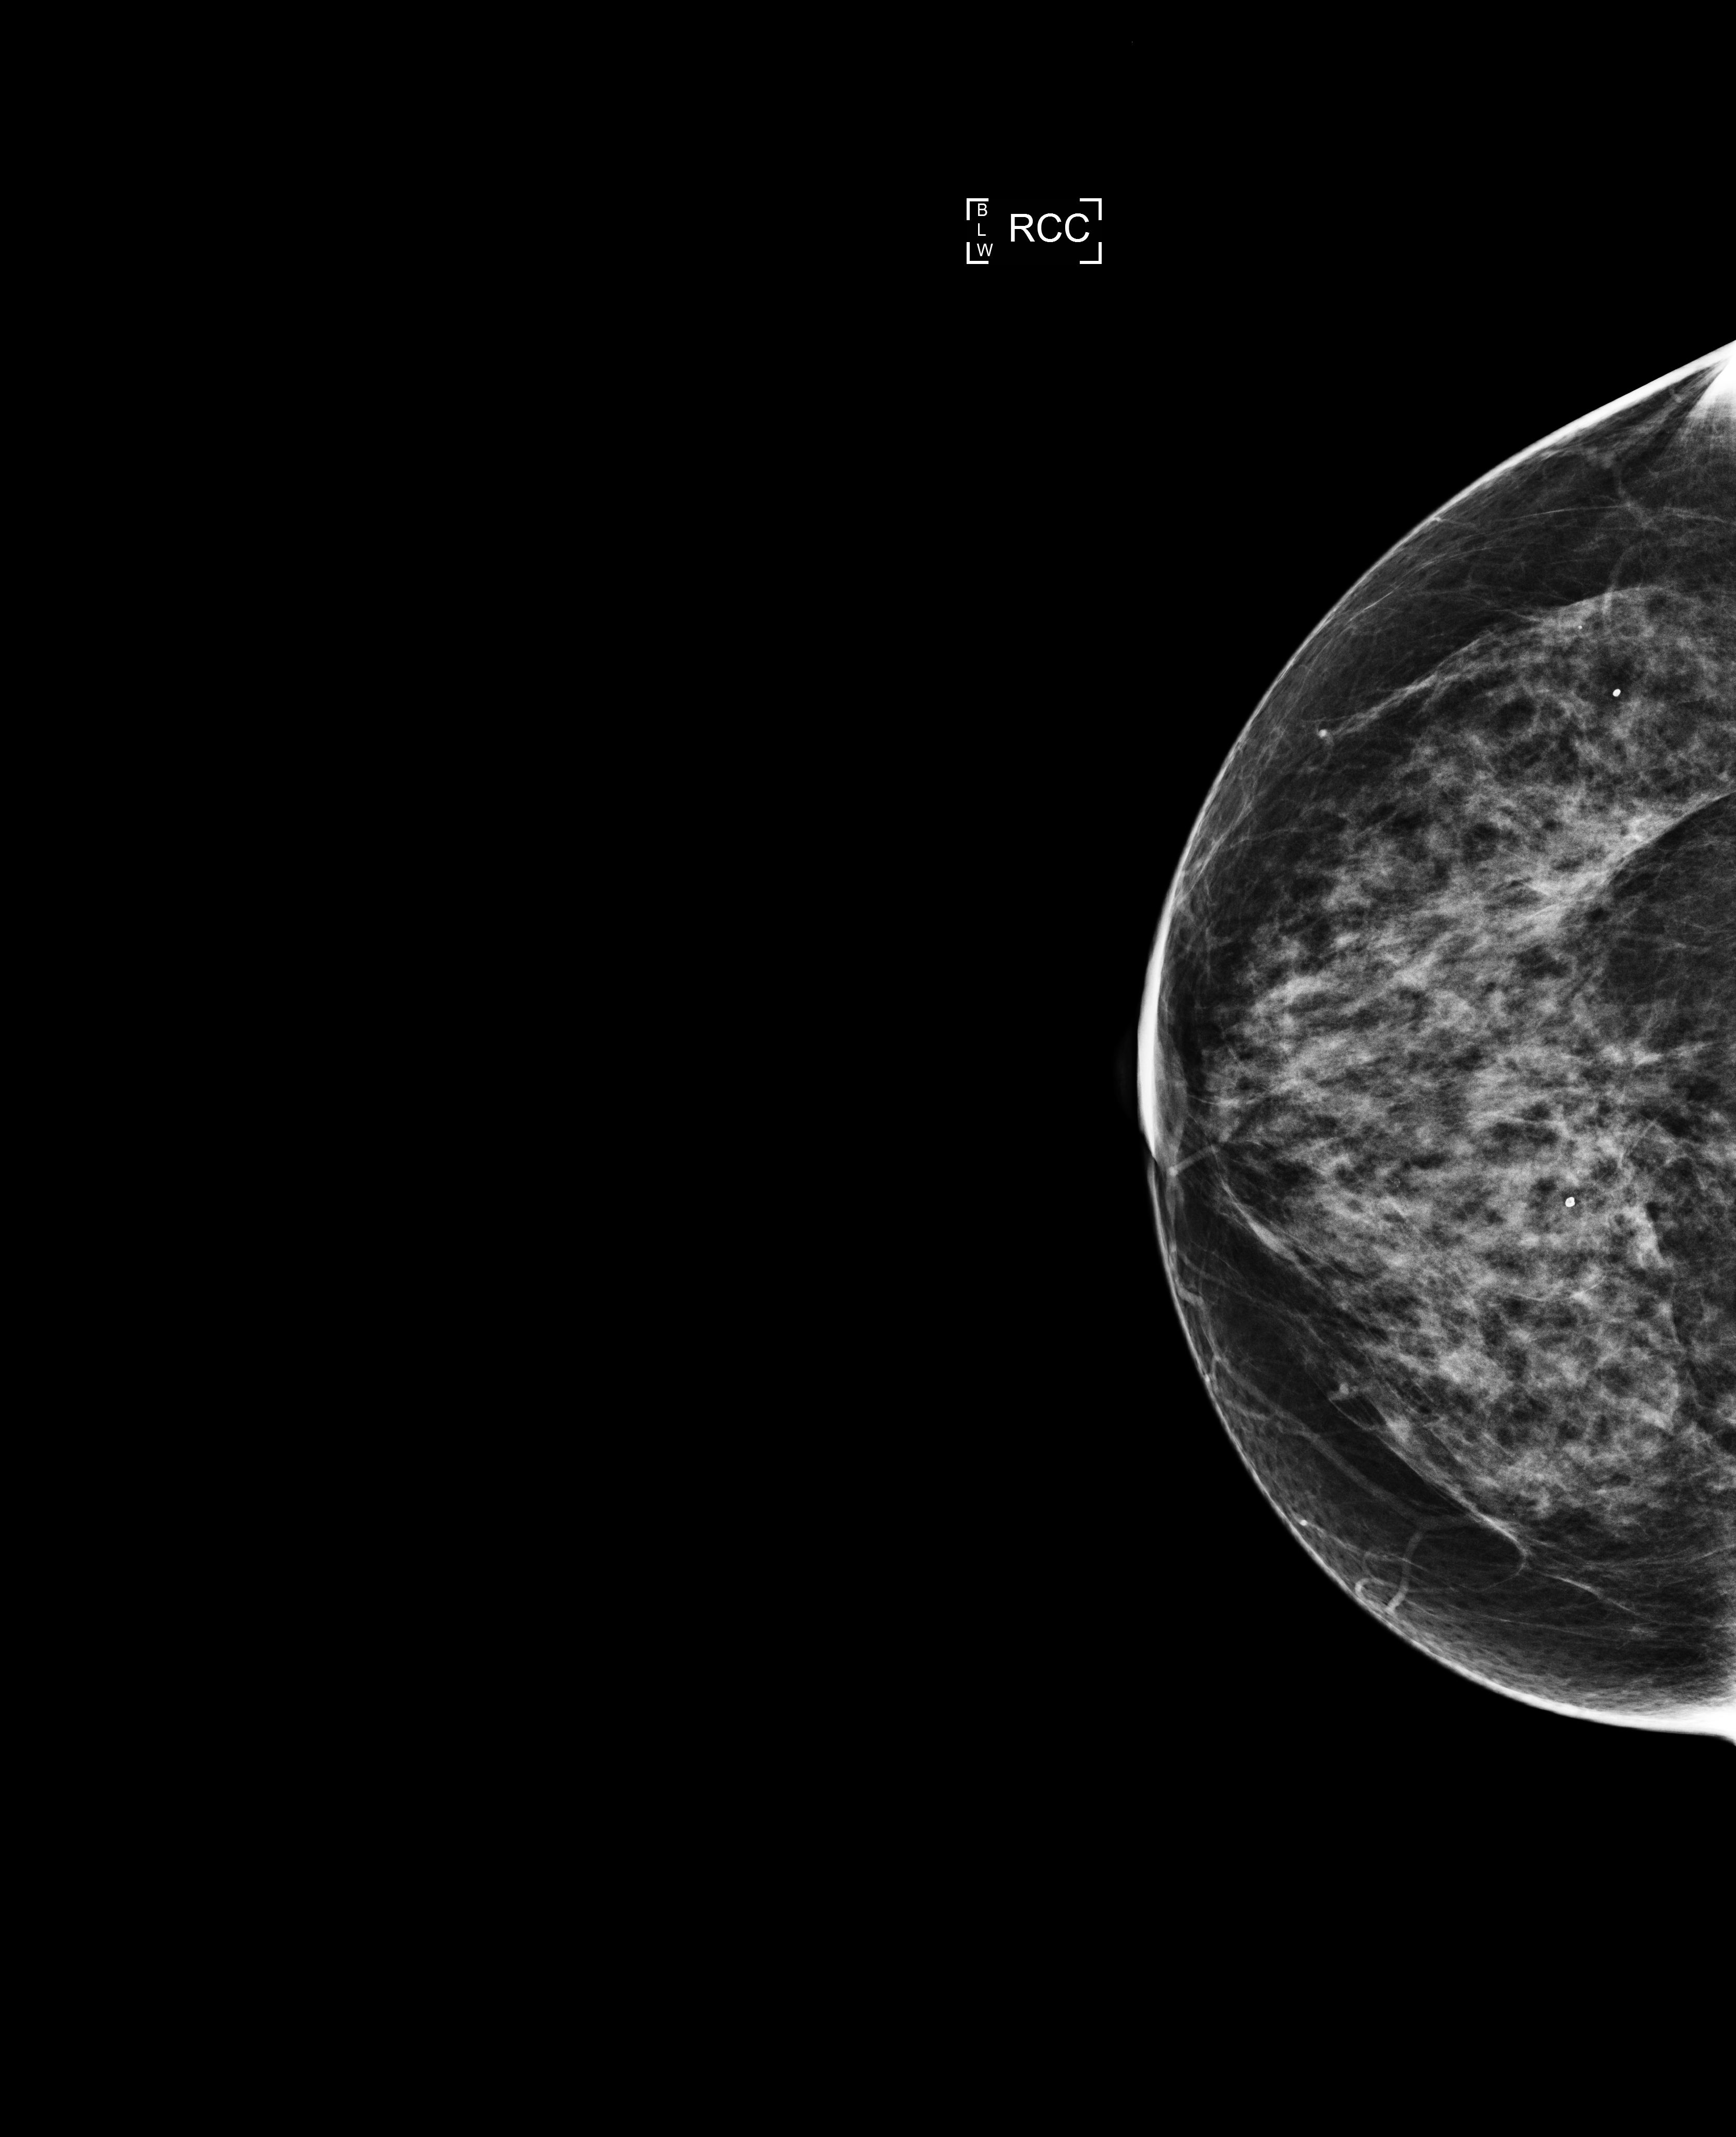
Digital mammogram (FFDM), right breast, craniocaudal (CC) view, screening examination, system: Selenia Dimensions. Patient aged 60 years (female).
BI-RADS breast density category at the screening exam (both breasts, scale 1–4): 3. Final BI-RADS category for the screening round (tomosynthesis exam, both breasts): category 2. Recall: no recall after this screen.